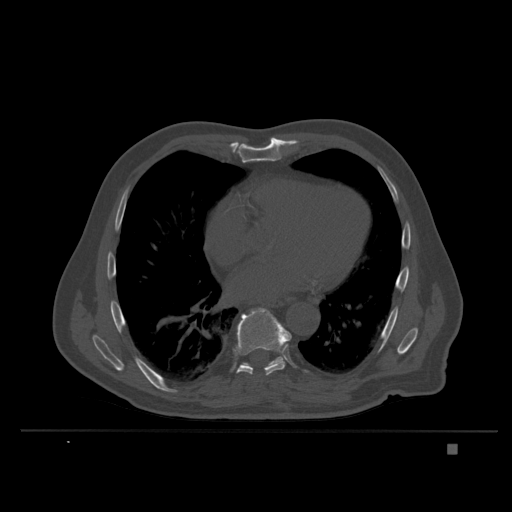
CT including the spine, one axial slice; position 226 of 435 along the scan axis; bone window (W 1800 / L 400 HU); 1.5 mm slice thickness; 512 × 512 image matrix, field of view 434 × 434 mm. Patient: male, 73 years. From the clinical record (not read from this slice): primary cancer: skin.
Structures marked on this image (semi-automatically segmented with operator editing):
- T8 vertebra: bounding box [x1, y1, x2, y2] px = [234, 308, 292, 376]
- T9 vertebra: [242, 357, 283, 368]